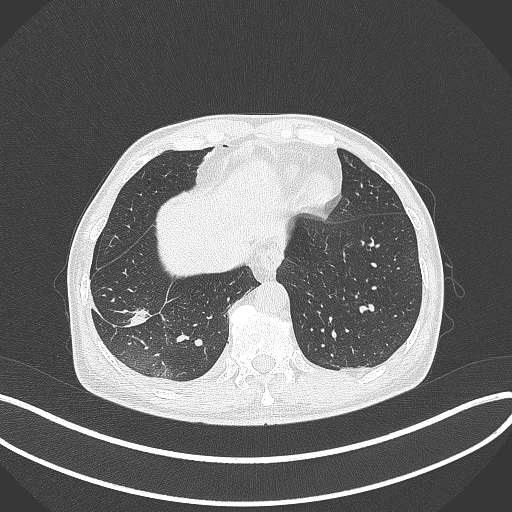
Chest CT, one axial slice. Slice 83 of 388 in the series (ordered by position). Reconstruction kernel B70f. Lung window (W 1500 / L -600 HU). 1 mm slice thickness. 512 × 512 image matrix, field of view 400 × 400 mm. Male patient, age 64 years. Case-level facts recorded for this patient, not image findings: clinical TNM (as recorded): T3 N0 M0; histopathological grade: G2-3.
Annotated regions visible in this slice (bounding box drawn by a radiologist):
- lung tumour (recorded histology: adenocarcinoma): bounding box (x1, y1, x2, y2) in pixels: (128, 304, 151, 327)